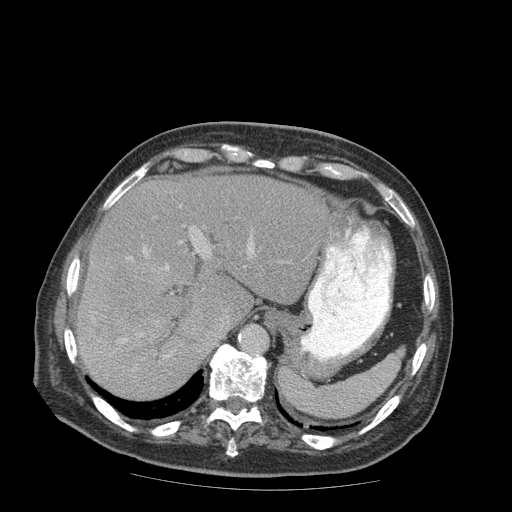
Contrast-enhanced abdominal CT (liver protocol), one axial slice; position 65 of 99 along the scan axis; reconstruction kernel STANDARD; soft-tissue window (W 400 / L 40 HU); 2.5 mm slice thickness; 512 × 512 image matrix, field of view 420 × 420 mm. Case-level facts recorded for this patient, not image findings: diagnosis: hepatocellular carcinoma (patient treated with transarterial chemoembolisation; whether this scan precedes or follows treatment is not stated here); TNM stage (as recorded): Stage-IIIB.
Outlined on this slice (semi-automatic segmentation, software-assisted and operator-edited):
- liver parenchyma outside the tumour (the mass and vessels are separate outlines, so this box may not span the whole liver): box from (x=78, y=174) to (x=336, y=398) px
- mass: (x=78, y=249)–(x=180, y=335)
- liver vessels: (x=121, y=187)–(x=254, y=358)